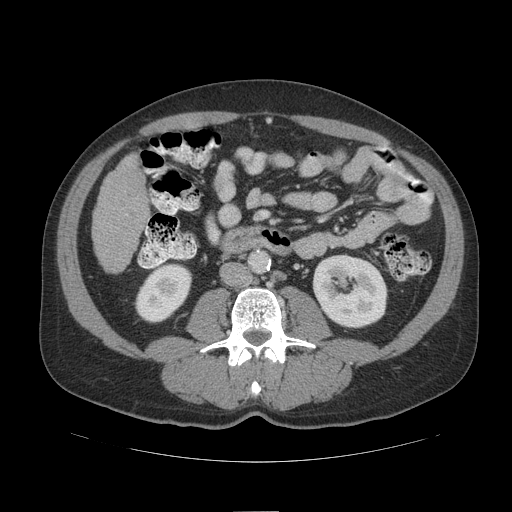
Contrast-enhanced abdominal CT (liver protocol), one axial slice. Slice 30 of 109 in the series (ordered by position). Reconstruction kernel STANDARD. Soft-tissue window (W 400 / L 40 HU). 2.5 mm slice thickness. 512 × 512 image matrix, field of view 420 × 420 mm. From the clinical record (not read from this slice): diagnosis: hepatocellular carcinoma (patient treated with transarterial chemoembolisation; whether this scan precedes or follows treatment is not stated here); TNM stage (as recorded): Stage-IIIB; Child-Pugh class: A.
Annotated regions visible in this slice (semi-automatic segmentation, software-assisted and operator-edited):
- liver parenchyma outside the tumour (the mass and vessels are separate outlines, so this box may not span the whole liver): bounding box (x1, y1, x2, y2) in pixels: (92, 154, 148, 272)